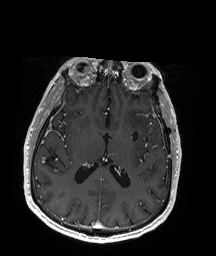
Brain MRI from a brain-tumour surgery series, one axial slice. Slice 90 of 192 in the series (ordered by position). T1-weighted post-contrast. 1 mm slice thickness. 216 × 256 image matrix. From the clinical record (not read from this slice): histopathology: Oligodendroglioma; WHO grade: 2; IDH mutation: yes; tumour location: Left Insular.
Outlined on this slice (expert manual segmentation):
- previous resection cavity: bounding box (x1, y1, x2, y2) in pixels: (137, 124, 158, 139)